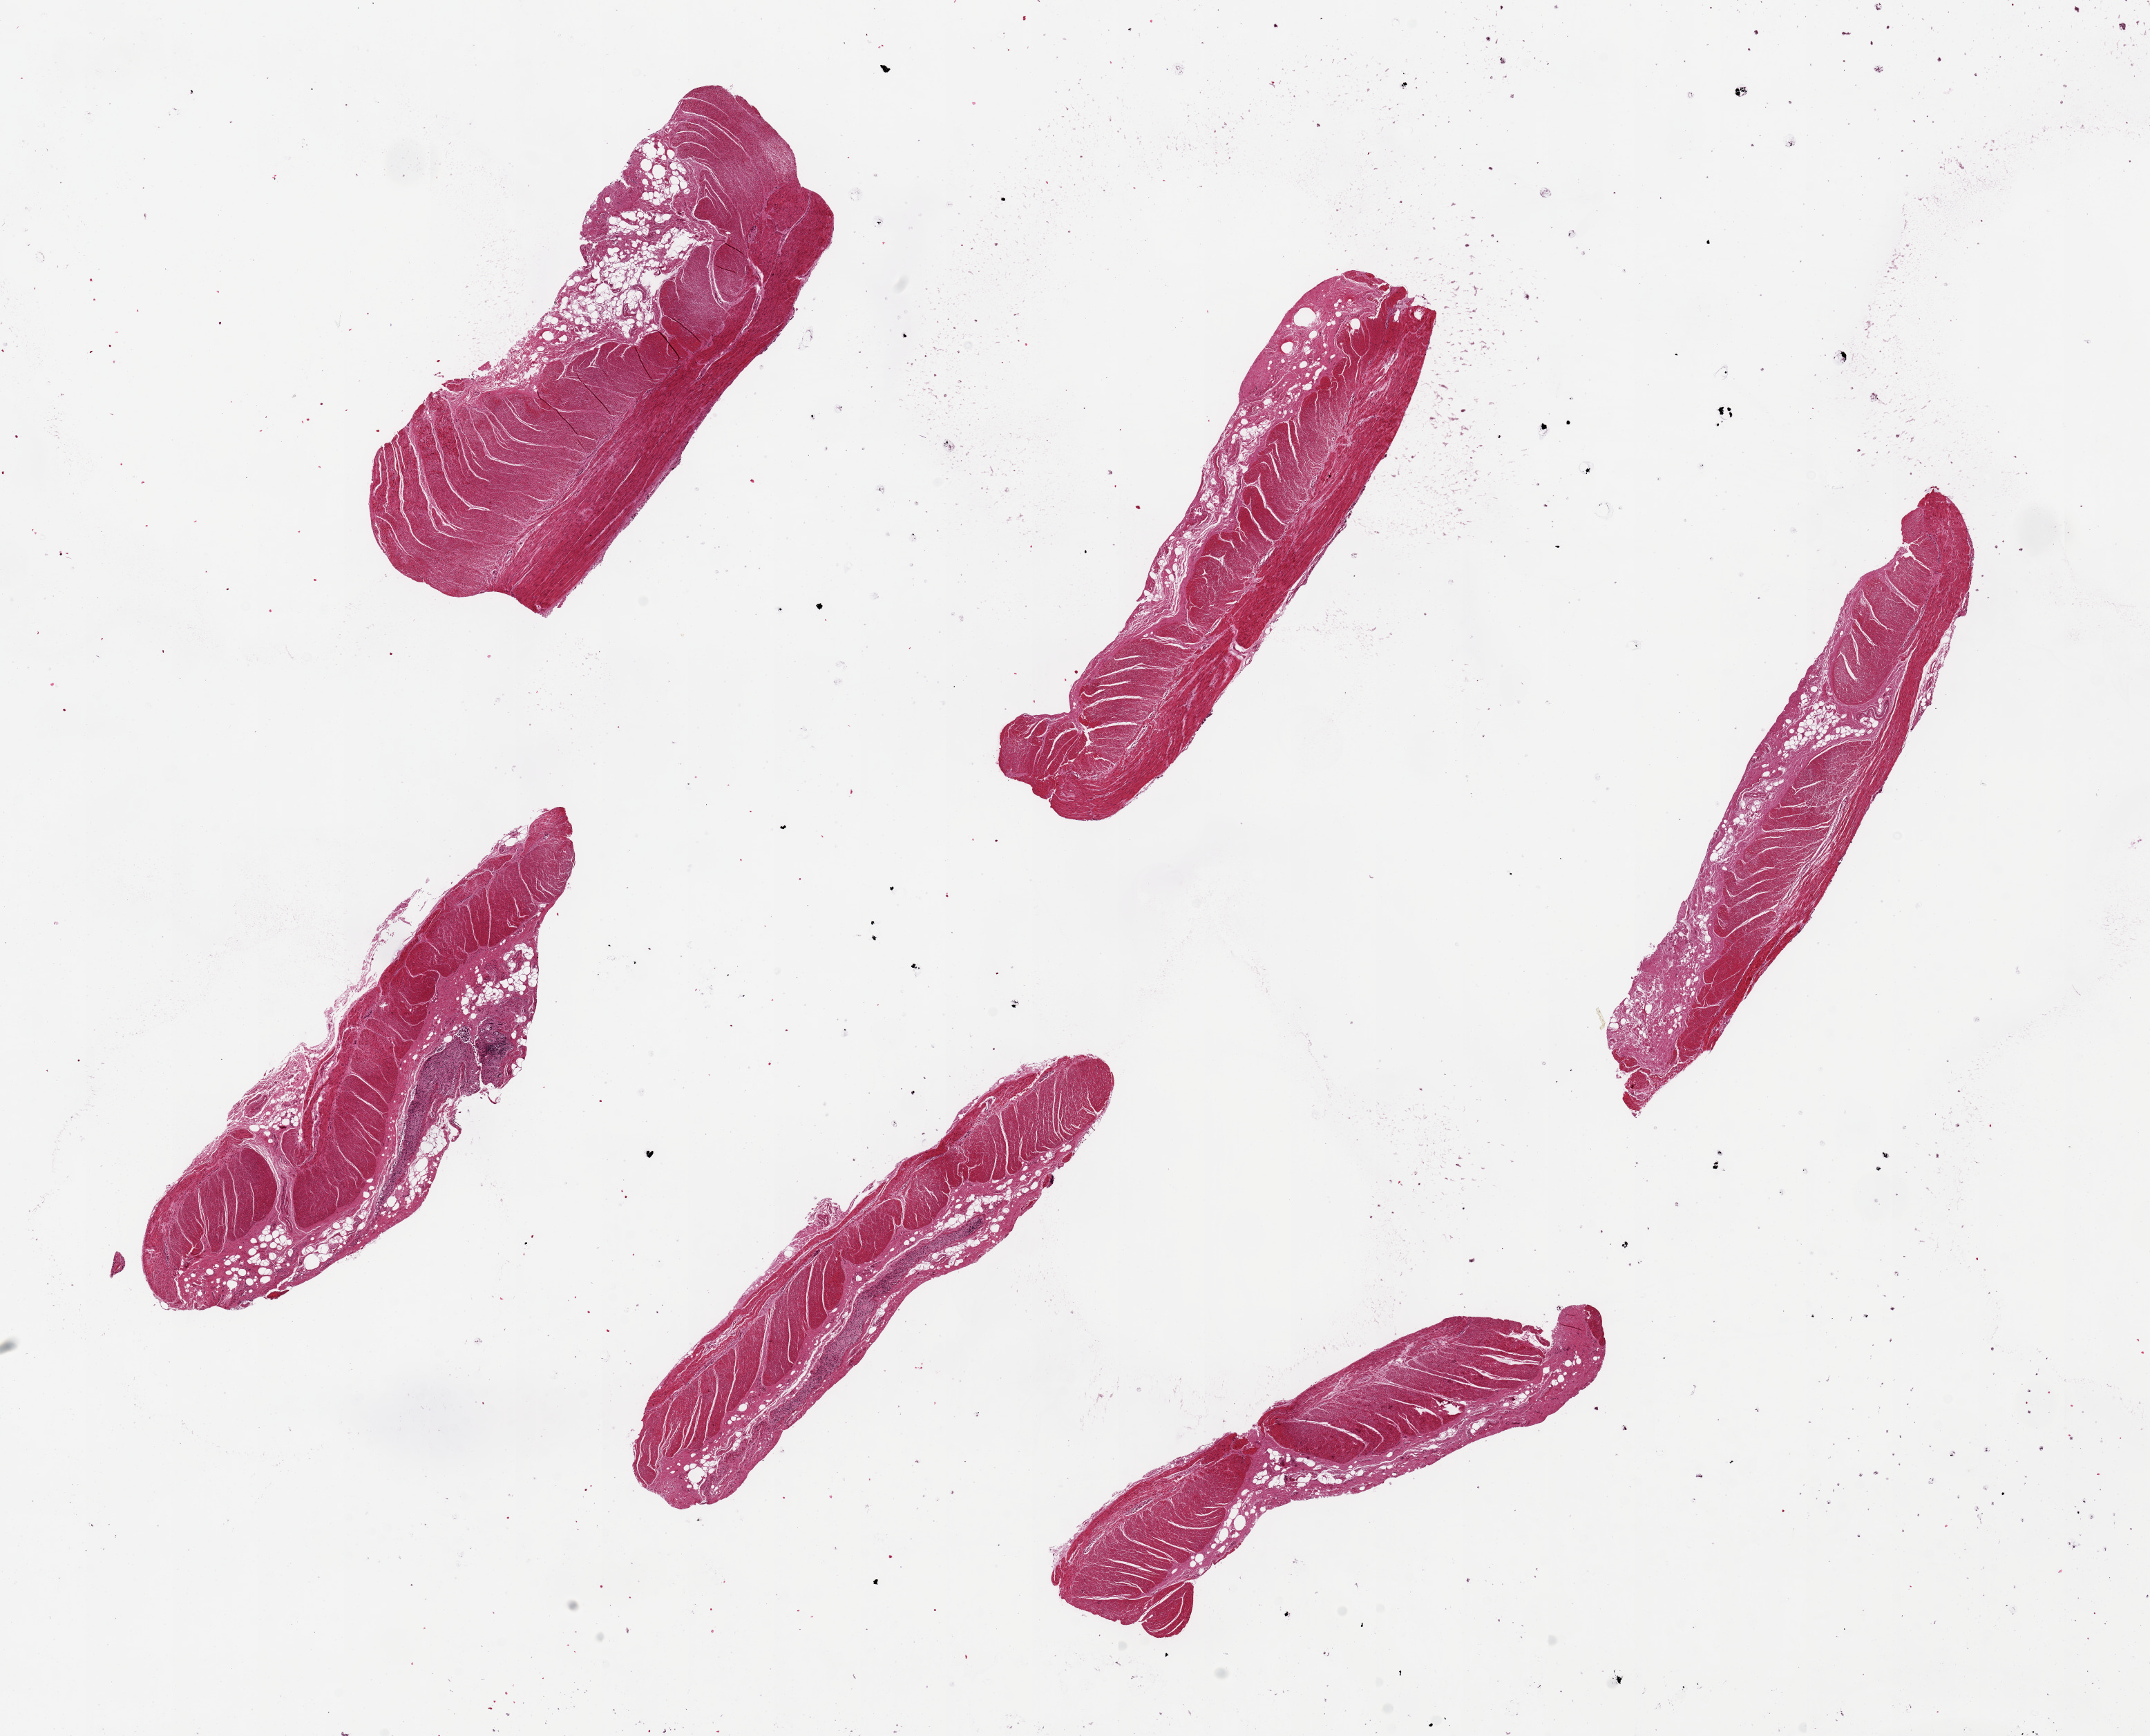
H&E whole-slide image, shown as a low-resolution overview of the whole scanned area (about 24.6 x 19.9 mm, slide scanned at 20x); PAXgene-fixed paraffin-embedded (PFPE) section; section of sigmoid colon (target tissue); donor tissue sample. Male donor.
Pathologist's review note for this sample: 6 pieces. up to 8x7.5mm; generally all muscularis, focal pigmented histiolcytic aggregate (? tattoo).